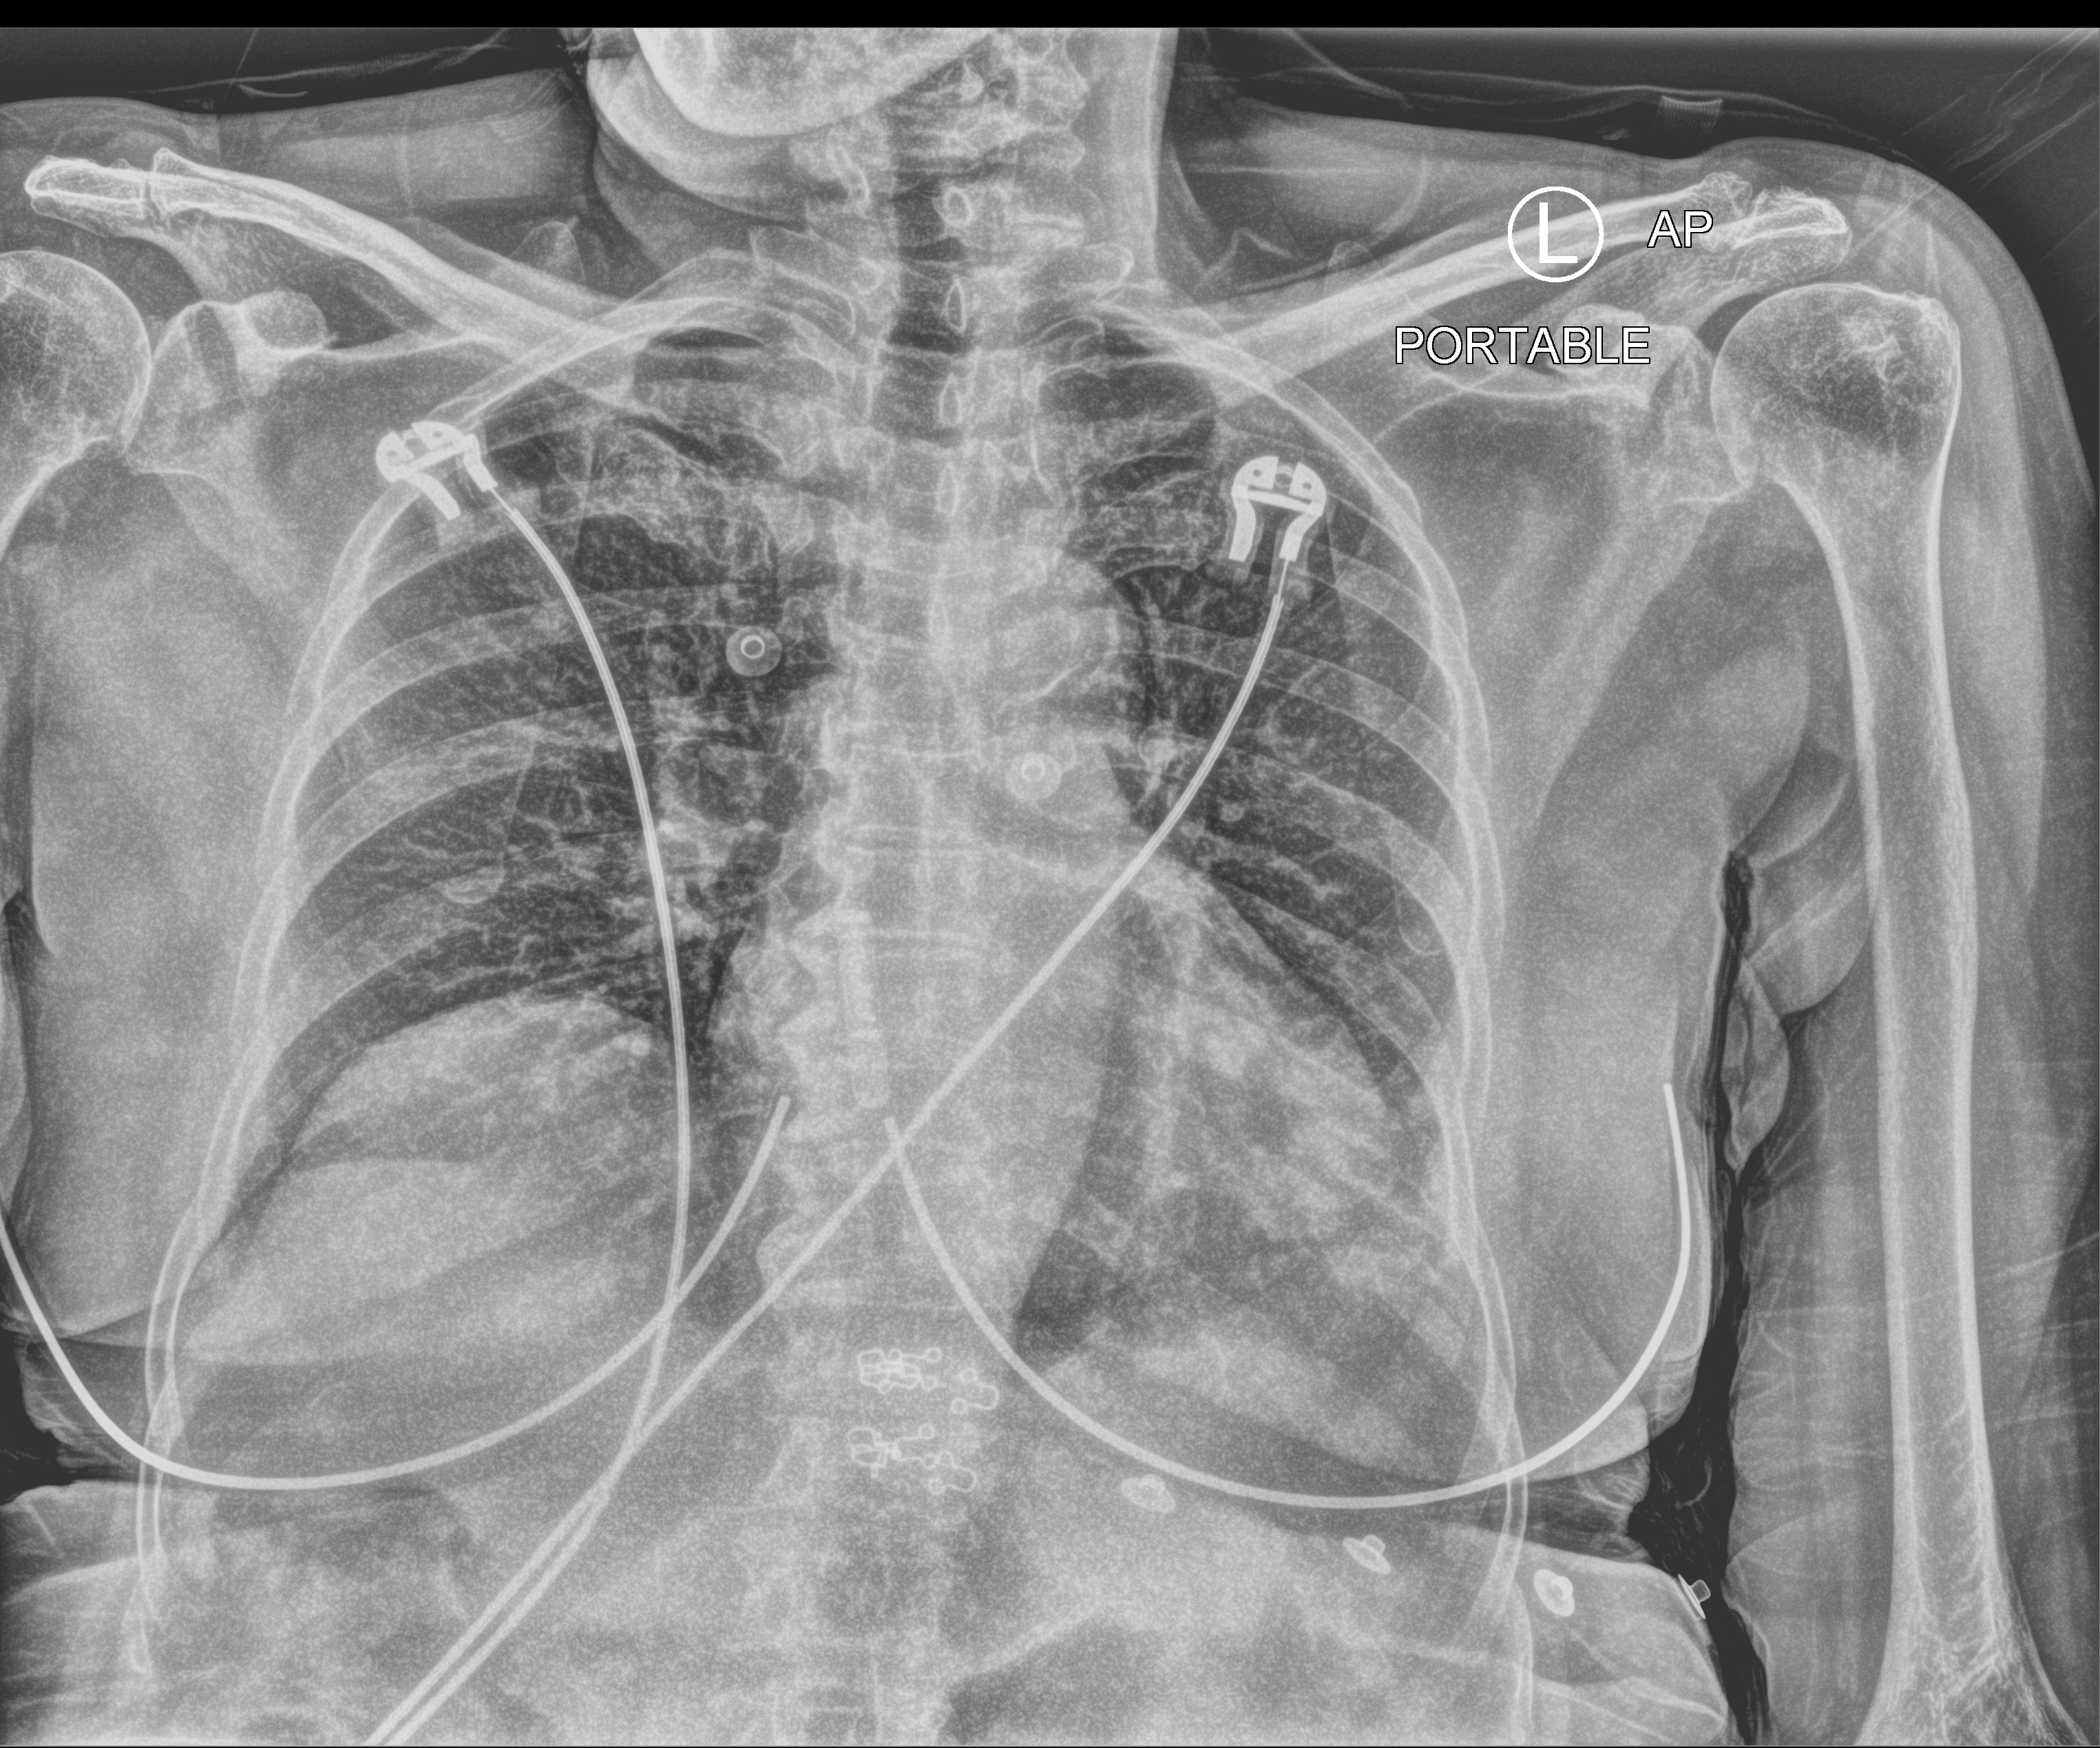
Chest X-ray (portable); anteroposterior (AP) projection. Female patient hospitalised with COVID-19, age 75–90 years.
Hospital-stay facts (about this admission, not read from this image; timing relative to this image not recorded):
- other chronic lung disease (admission record): no
- admitted to intensive care during this hospital stay: no